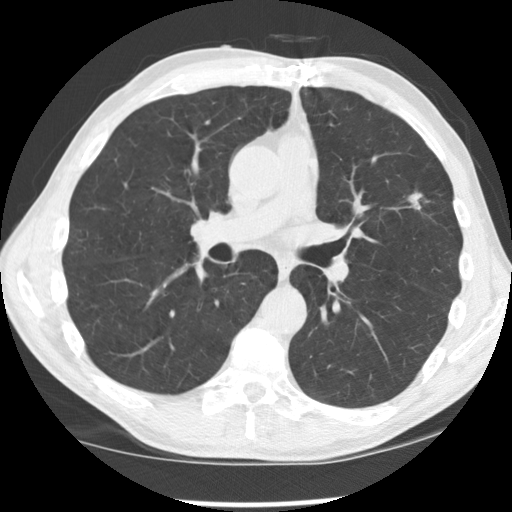
Low-dose screening chest CT, one axial slice. Slice 96 of 170 in the series (ordered by position). Reconstruction kernel STANDARD. Lung window (W 1500 / L -600 HU). 2.5 mm slice thickness. 512 × 512 image matrix, field of view 340 × 340 mm.
Structures marked on this image (outlined manually by an expert reader):
- lesion 1 (tumor, upper lobe of left lung): bounding box (x1, y1, x2, y2) in pixels: (405, 192, 423, 210)